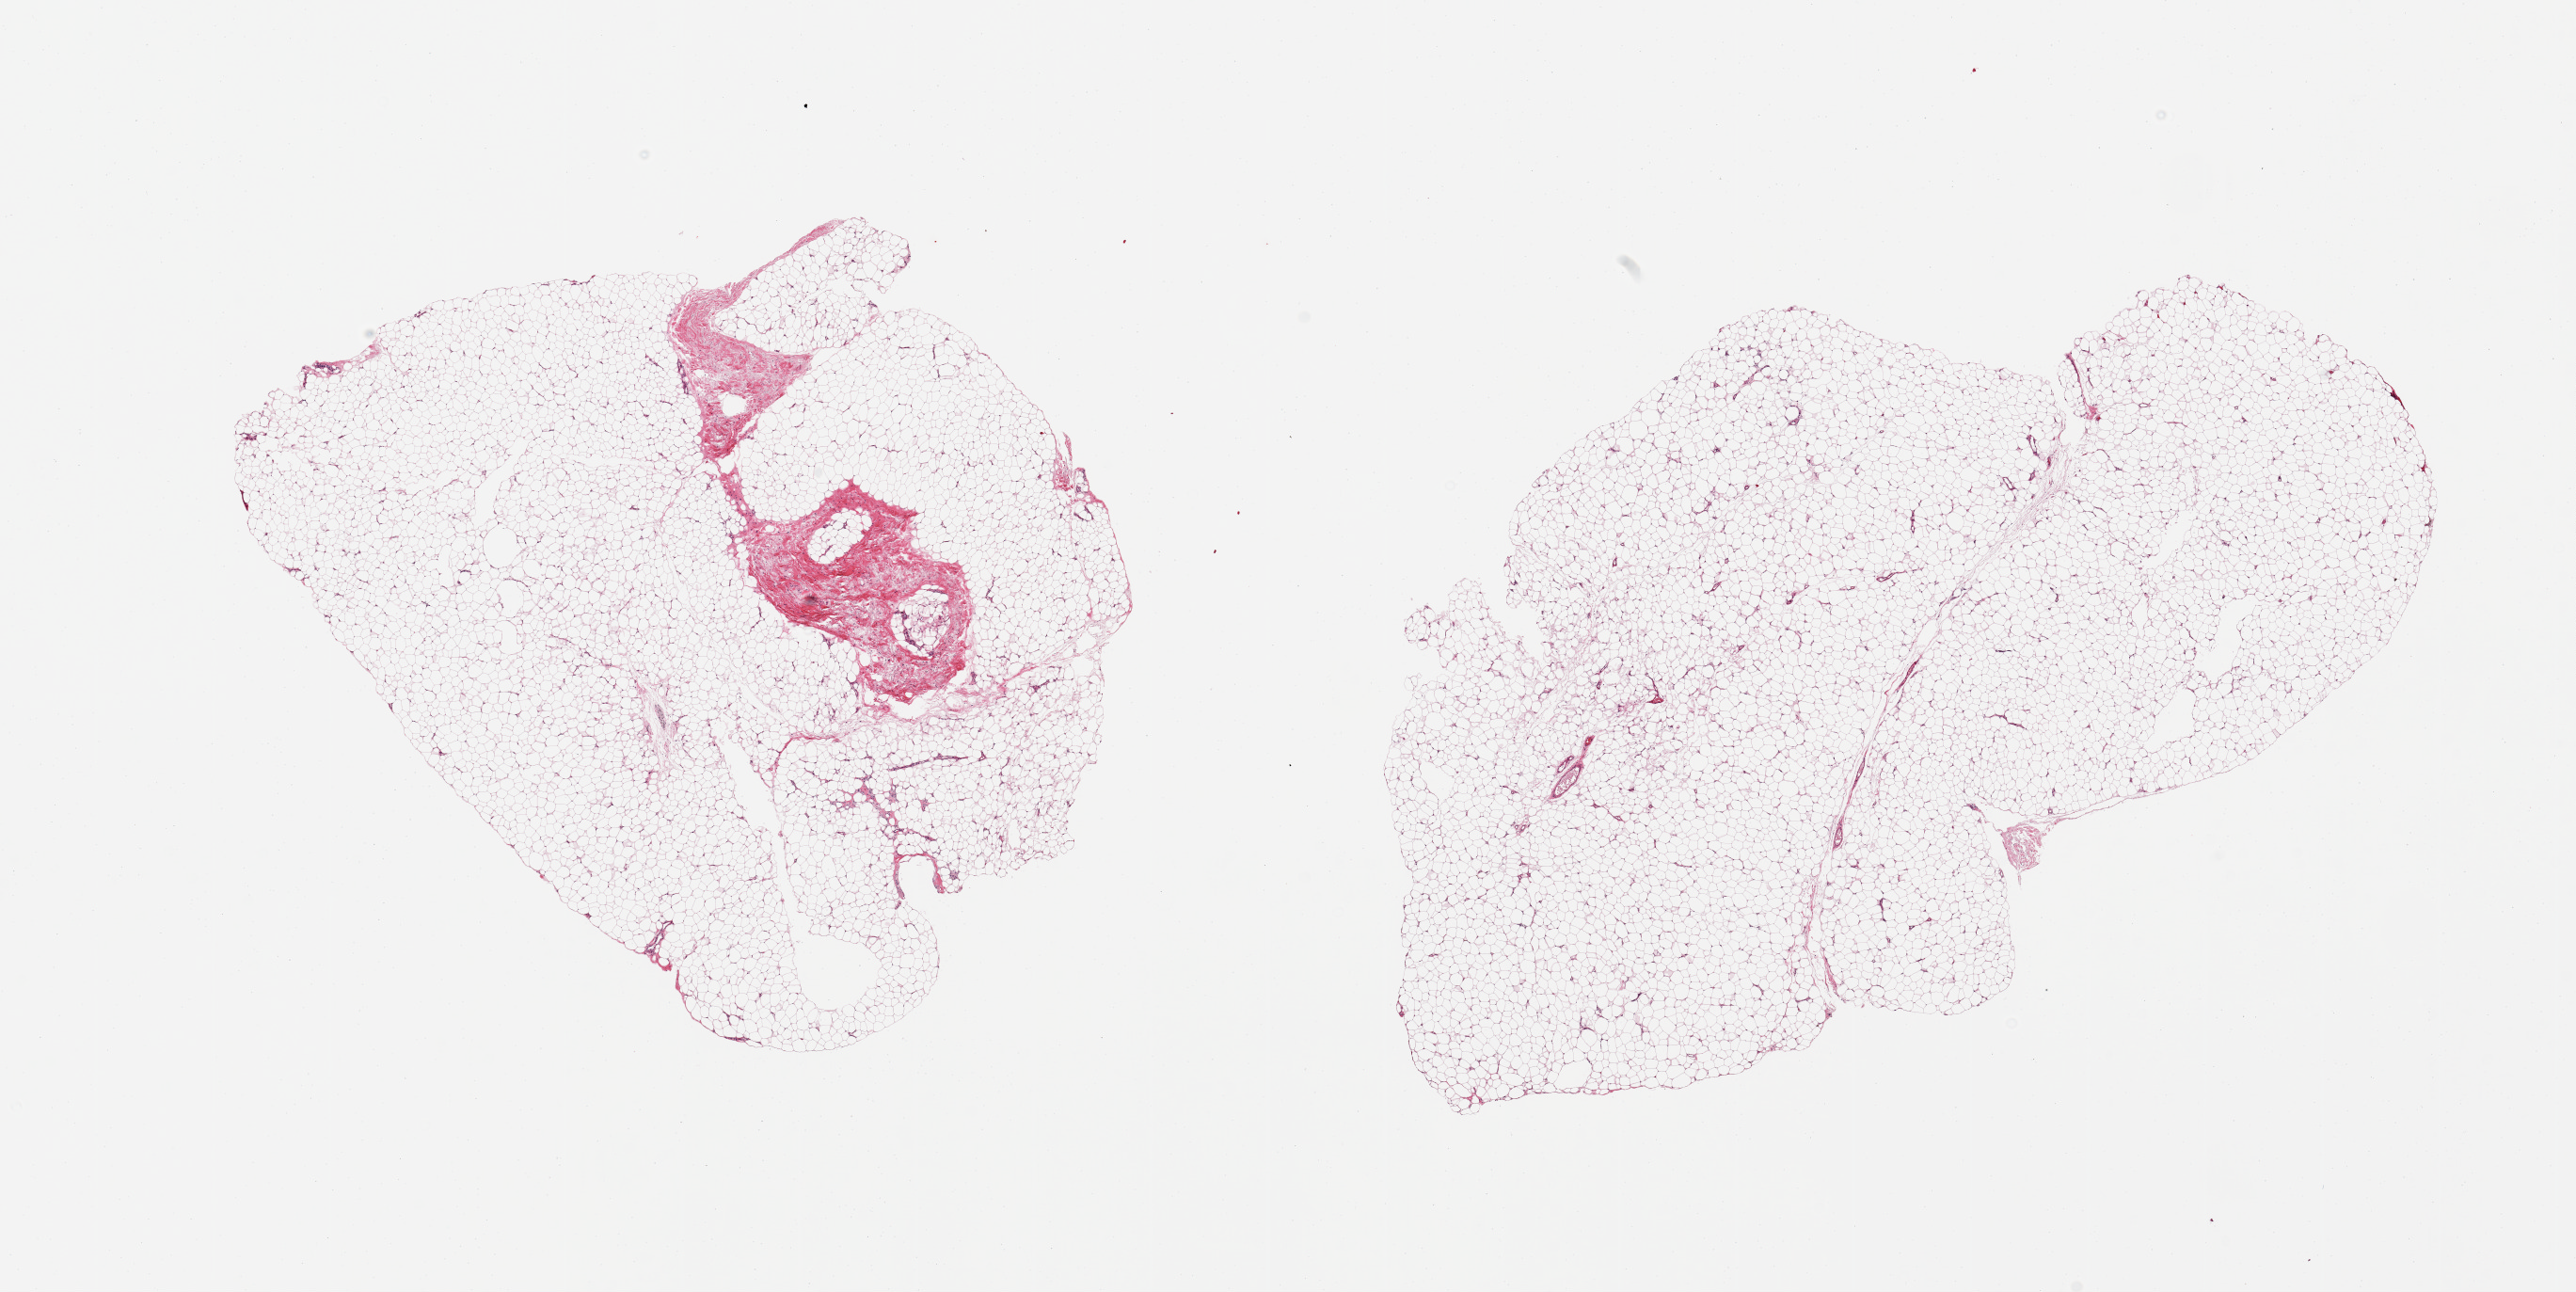
Haematoxylin and eosin whole-slide image, a low-resolution overview of the entire scanned area, about 21.7 x 10.9 mm (slide scanned at 20x). PAXgene-fixed, paraffin-embedded tissue. Sampled site (target tissue): adipose tissue. Donor tissue sample.
Reviewer comment on this tissue sample: 2 pieces; stroma 10% in 1, none in other.